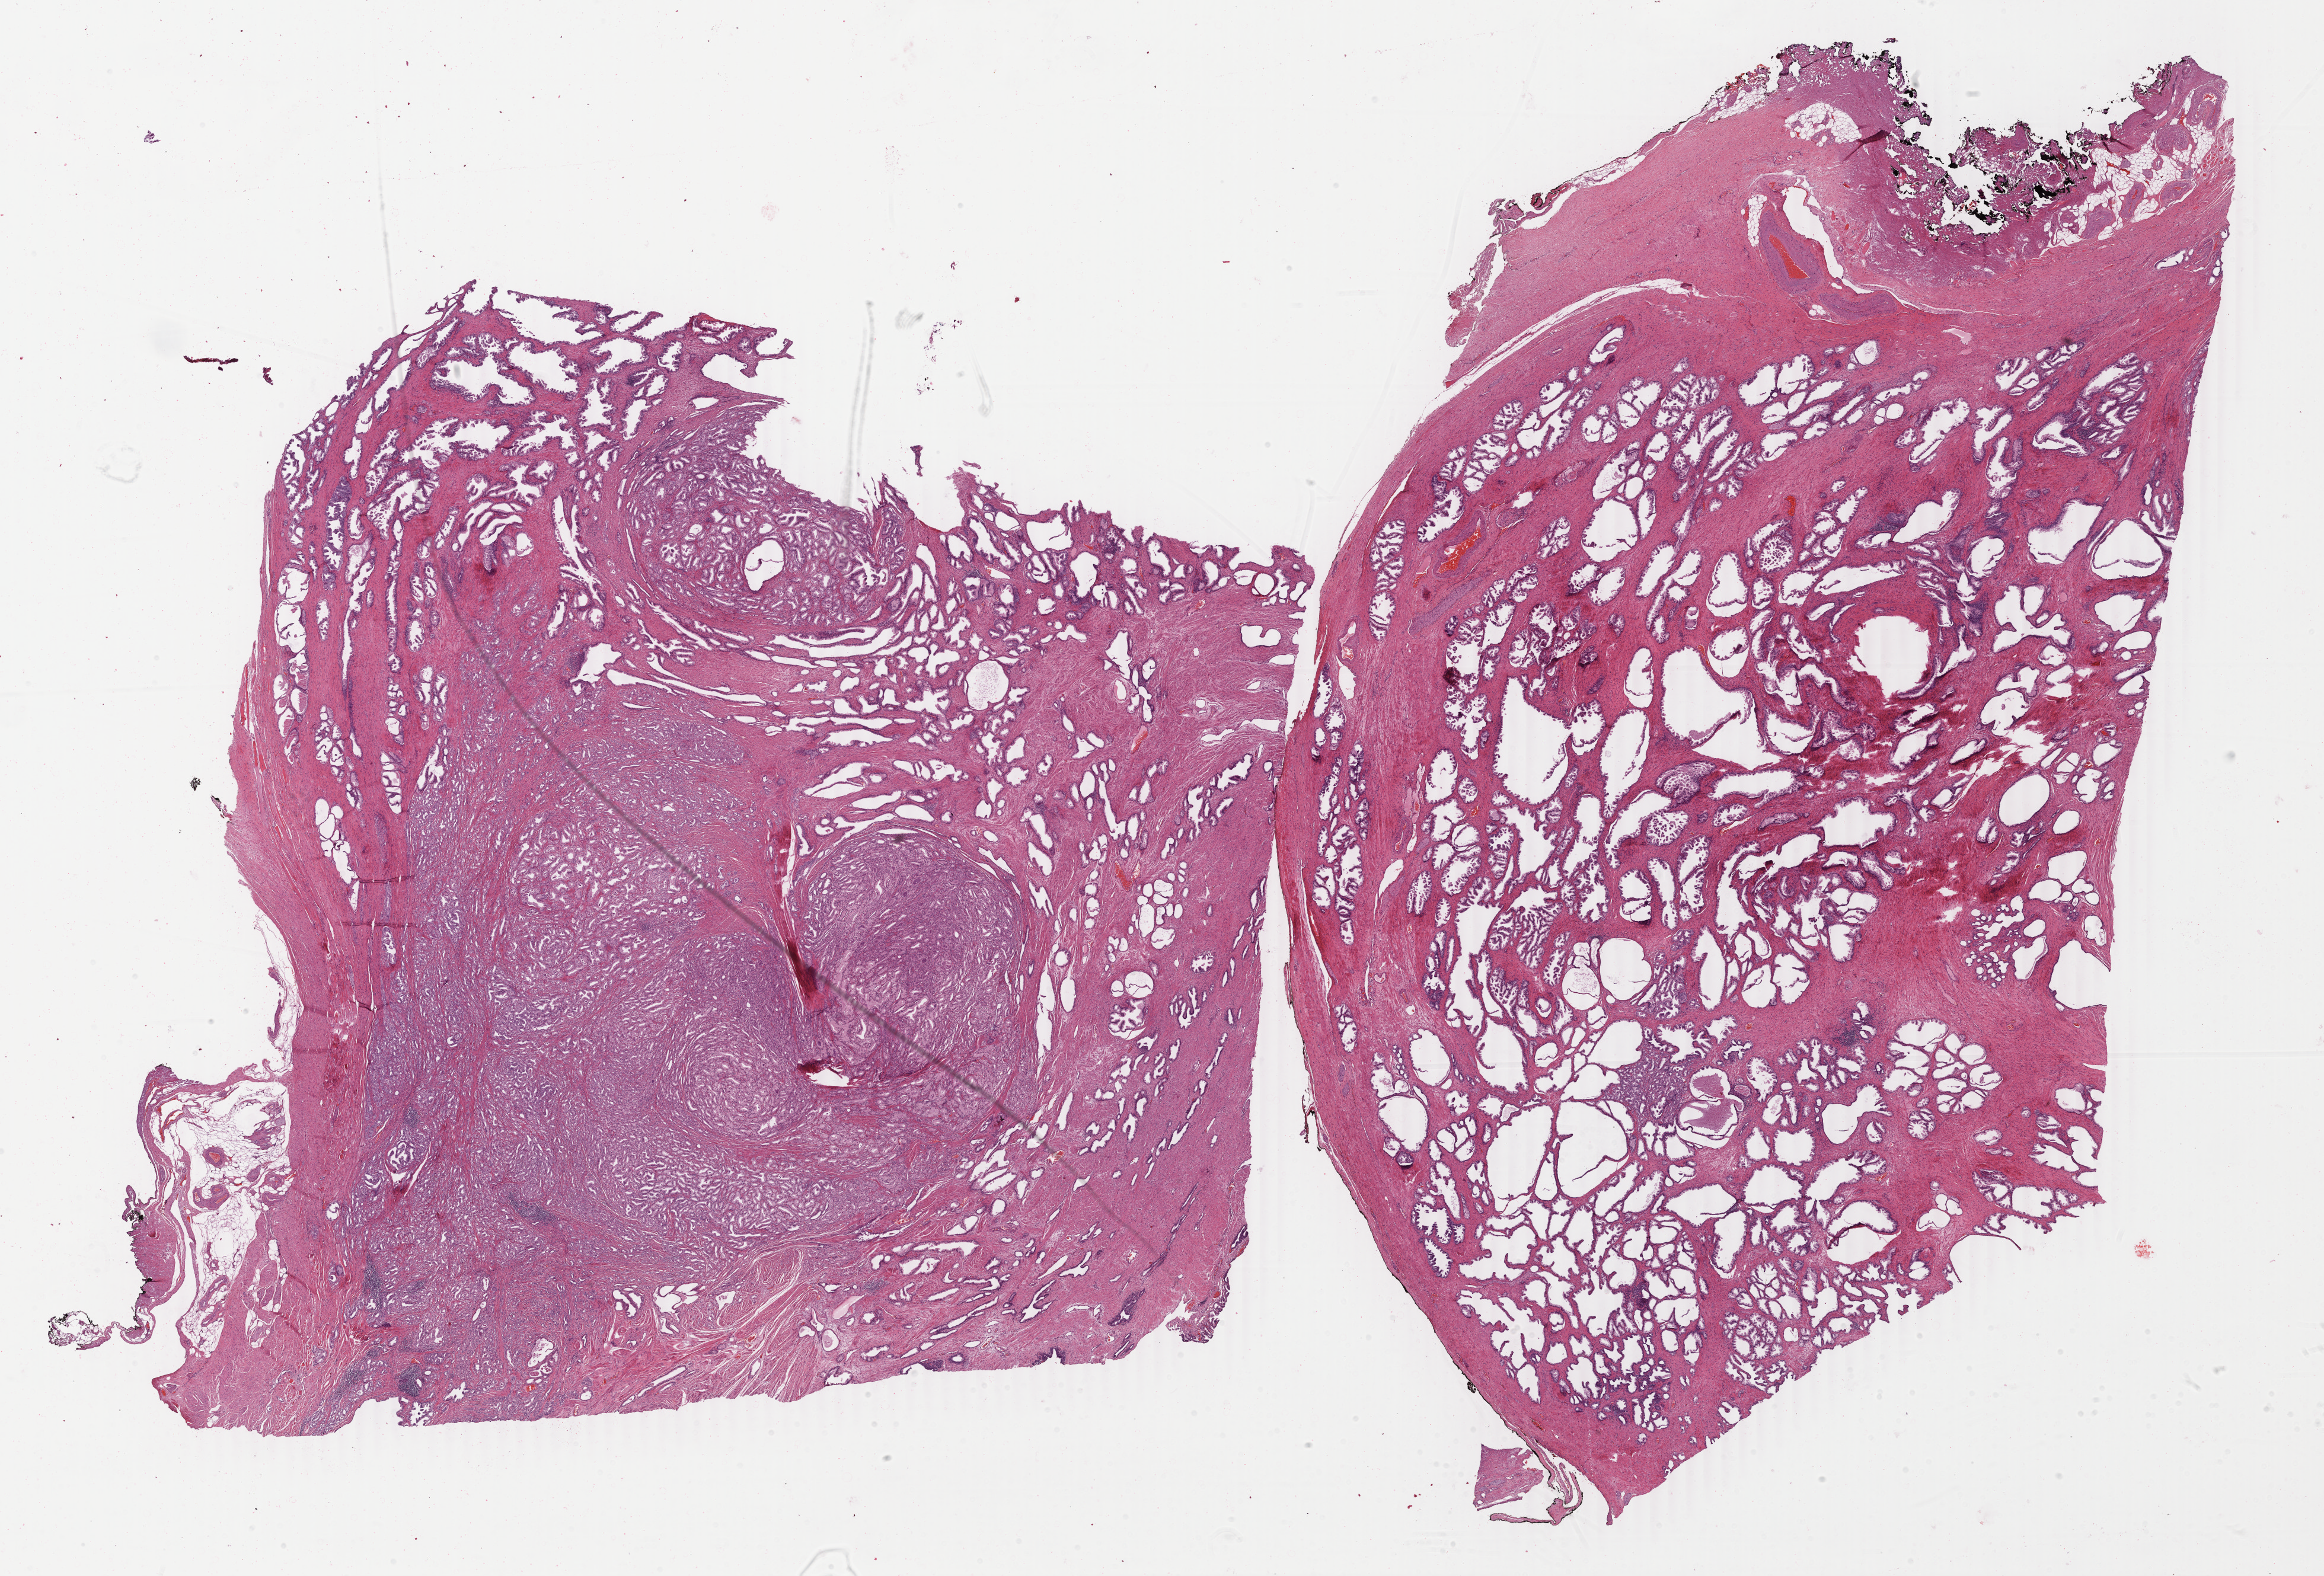
Whole-slide histology image, H&E, low-resolution overview of the scanned area, about 31.2 x 21.1 mm (slide scanned at 40x); formalin-fixed paraffin-embedded (FFPE) diagnostic section; sample: primary tumour, prostate. Male, age 77 years at initial diagnosis.
Diagnosis: Adenocarcinoma, NOS (prostate gland).